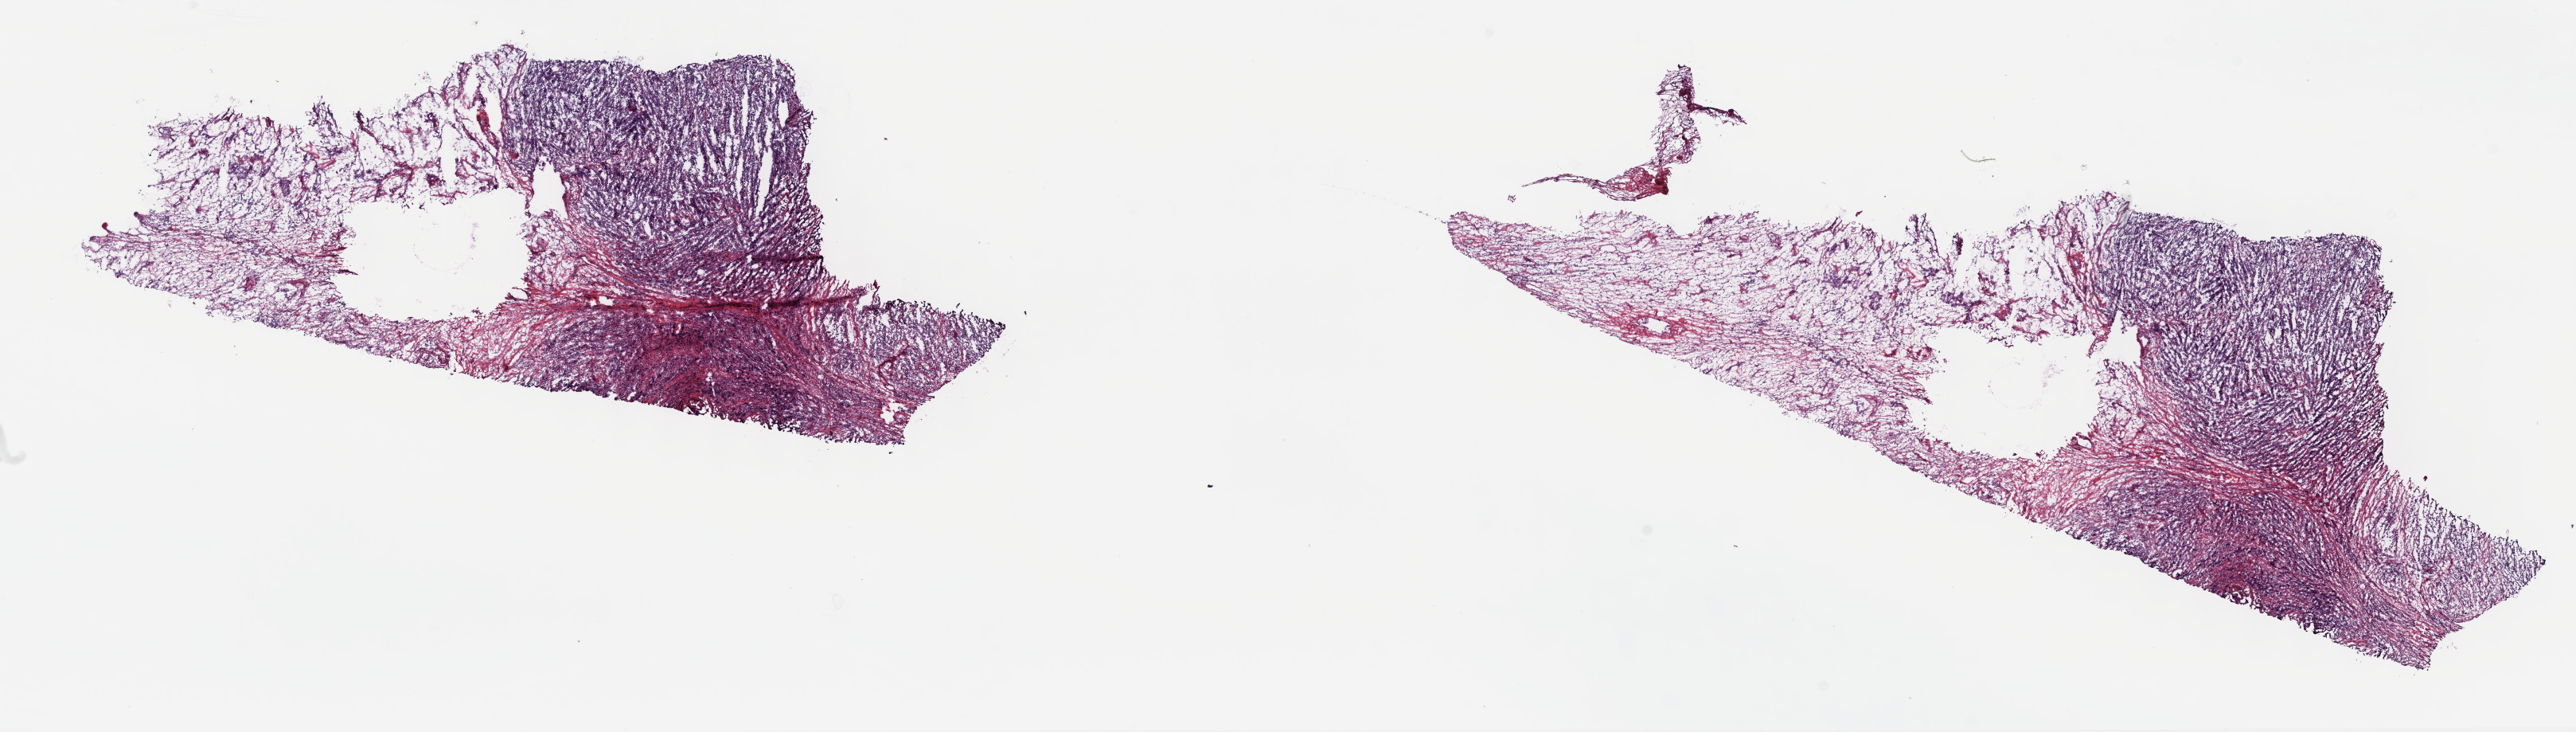
Whole-slide histology image, H&E-stained — low-resolution overview of the scanned area, about 26.2 x 7.4 mm, frozen section, sample: primary tumour, testis. Male patient; age at initial diagnosis 39 years. Slide review estimates, as recorded: tumour cells 70%, tumour nuclei 70%, normal cells 0%, stromal cells 30%, necrosis 0%. Inflammatory infiltration, as recorded: lymphocyte infiltration 5%, monocyte infiltration 0%, neutrophil infiltration 0%.
Laterality: right. Diagnosis: Mixed germ cell tumor. AJCC pathologic stage: IB (6th edition).